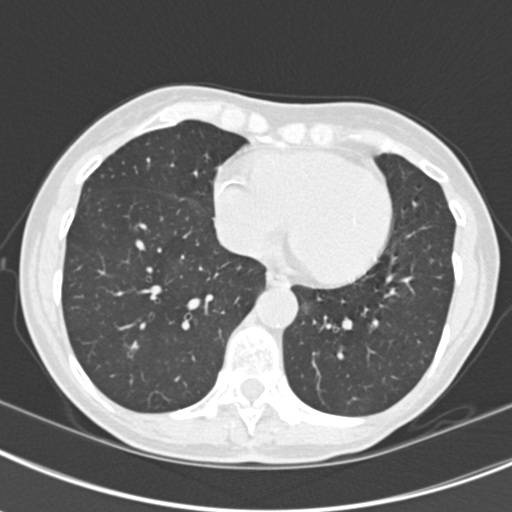
Low-dose screening chest CT, axial slice, second annual screen, lung window (W 1500 / L -600 HU), 2 mm slice thickness, standard (soft-tissue) reconstruction kernel (B30f), 120 kVp, slice 133 of 219 in the series. Female, age 63 years at enrolment. Current smoker at enrolment.
Lesion marked by an expert reader, bounding box [x1, y1, x2, y2] px = [111, 327, 154, 370]. The screening reader recorded 9 non-calcified nodules or masses ≥4 mm on this exam (left upper lobe, right upper lobe, left upper lobe, left lower lobe, right middle lobe, left lower lobe, left lower lobe, right lower lobe, right lower lobe); which of them this box marks is not recorded. Official screen result: positive, other. Participant outcome: lung cancer diagnosed 408 days after this screen (after the third annual screen) — bronchiolo-alveolar adenocarcinoma, NOS, right upper lobe, right middle lobe, right lower lobe, left upper lobe, left lower lobe, moderately differentiated (G2), stage IV (AJCC 6th edition).